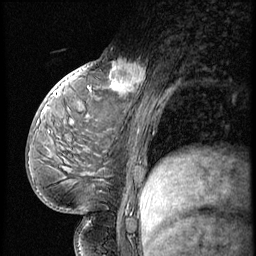
Breast MRI (dynamic contrast-enhanced), one sagittal slice. Position 29 of 56 along the scan axis. 3 images stored at this slice position (order not interpretable as contrast timing). 1.5 T. TE 4.2 ms, TR 9 ms. 256 × 256 image matrix, field of view 180 × 180 mm. Patient: female, 54 years. Case-level facts recorded for this patient, not image findings: setting: breast cancer imaged before/during neoadjuvant chemotherapy; receptor status: triple-negative.
Outlined on this slice (semi-automatic segmentation, software-assisted and operator-edited):
- analysis volume of interest (the breast-tissue region the enhancement analysis was run in; not a lesion): bounding box [x1, y1, x2, y2] px = [99, 53, 149, 102]
- tumour enhancement mask (voxels above the 140 % enhancement threshold inside the analysis volume of interest): [110, 61, 145, 93]